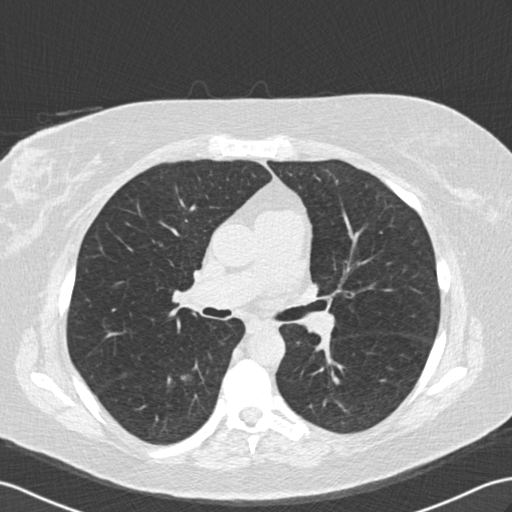
Low-dose screening chest CT, one axial slice; slice 91 of 154 in the series (ordered by position); lung window (W 1500 / L -600 HU); 2 mm slice thickness; 512 × 512 image matrix.
Annotated regions visible in this slice (manually delineated by an expert):
- lesion 1 (tumor, lower lobe of right lung): box from (x=180, y=373) to (x=194, y=383) px